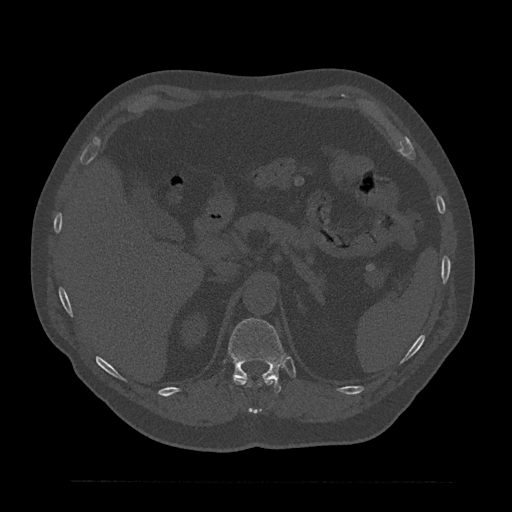
CT including the spine, one axial slice; slice 255 of 797 in the series (ordered by position); reconstruction kernel Br40s/3; 120 kVp; bone window (W 1800 / L 400 HU); 0.5 mm slice thickness; 512 × 512 image matrix, field of view 430 × 430 mm. Male patient, age 61 years. Case-level facts recorded for this patient, not image findings: primary cancer: prostate.
Structures marked on this image (semi-automatic segmentation, software-assisted and operator-edited):
- T11 vertebra: bounding box [x1, y1, x2, y2] px = [233, 377, 275, 414]
- T12 vertebra: [228, 318, 285, 393]